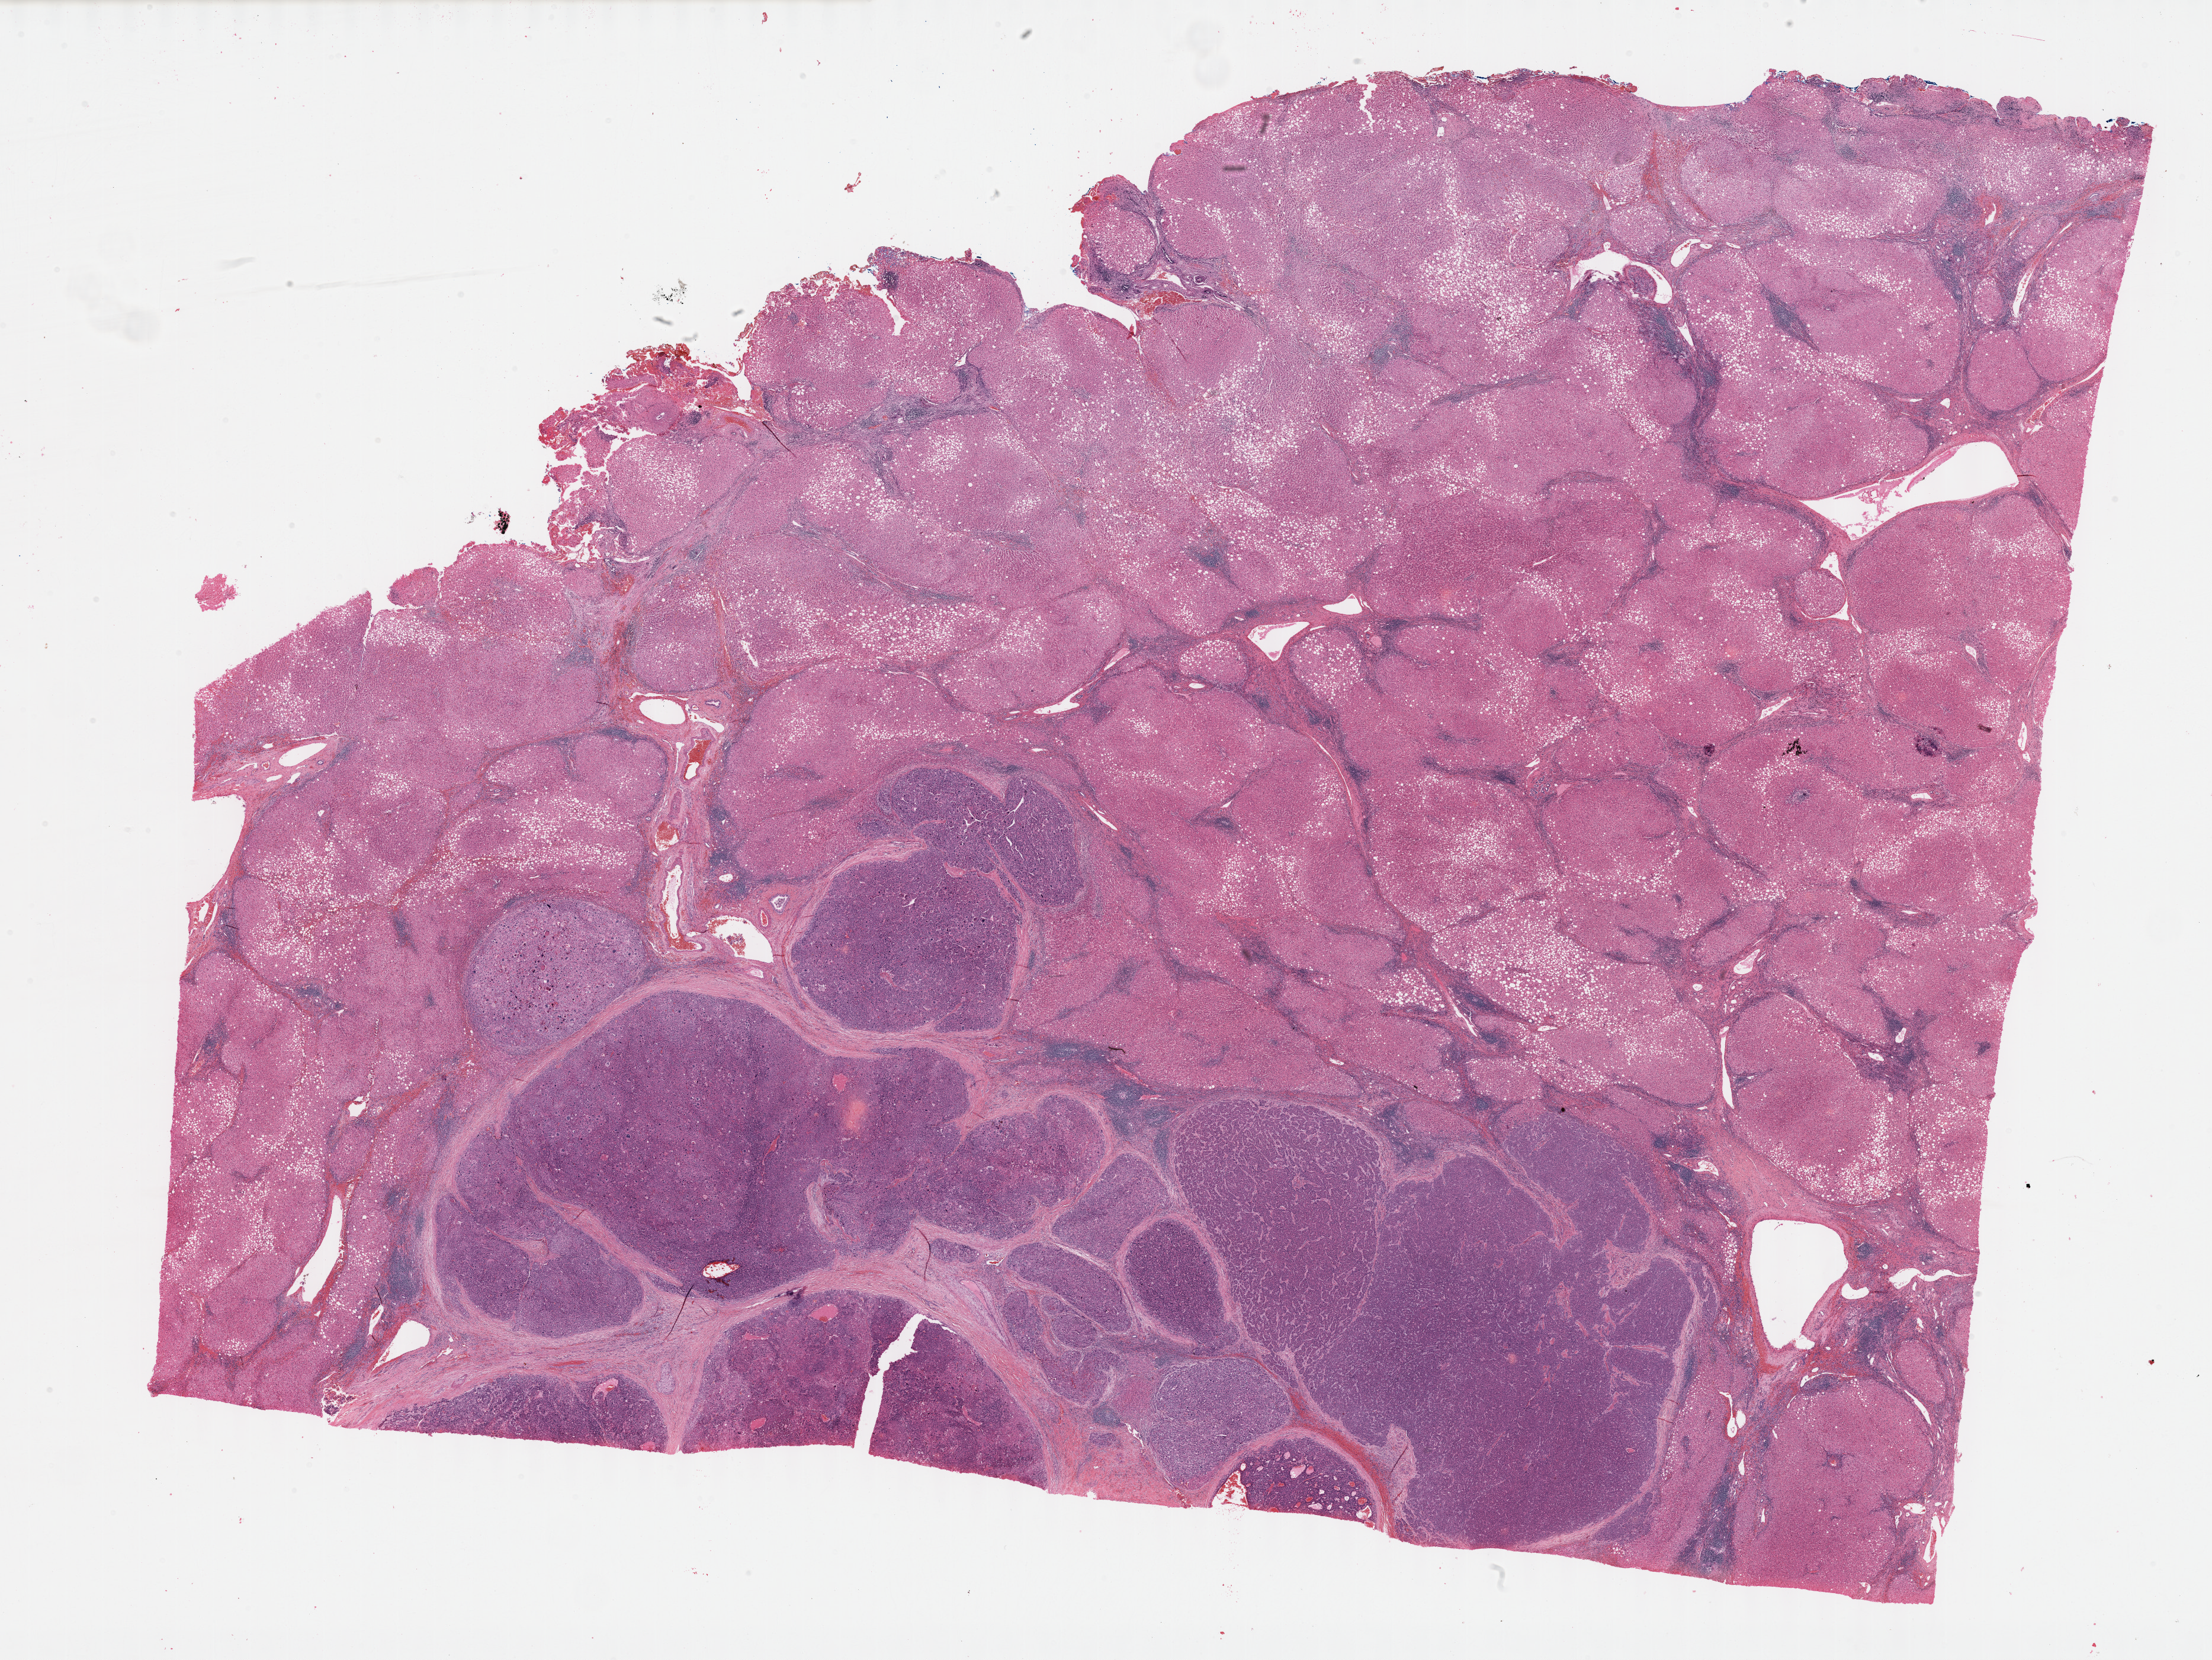
Whole-slide histology image, H&E — a low-resolution overview of the entire scanned area, about 30.2 x 22.6 mm. Formalin-fixed paraffin-embedded (FFPE) diagnostic section. Liver, primary tumour sample. Patient: male, age at initial diagnosis 58 years. Histologic grade: G2 (moderately differentiated).
Pathologic diagnosis: Hepatocellular carcinoma, NOS. AJCC pathologic stage: I.